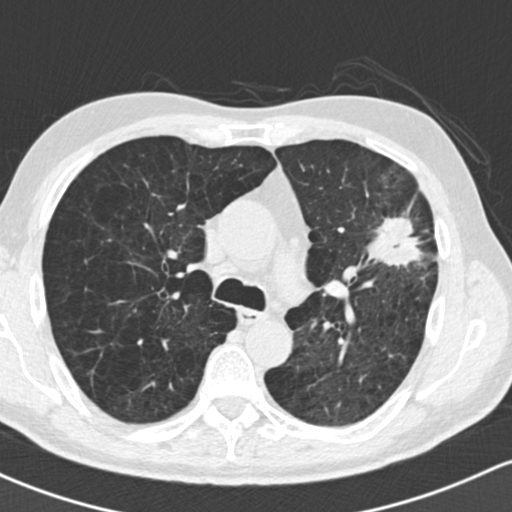
Chest CT (low-dose screening protocol), one axial image. First (baseline) screen. Lung window (W 1500 / L -600 HU). 2 mm slice thickness. Standard (soft-tissue) reconstruction kernel (B30f). Slice 62 of 162 in the series. Male participant, aged 61 years at enrolment. Former smoker at enrolment.
Expert reader's lesion annotation, box from (x=356, y=186) to (x=454, y=294) px. Screening reader's record for this exam (one nodule recorded; not confirmed to be the boxed lesion): non-calcified nodule or mass ≥4 mm, left upper lobe, 35 × 35 mm, spiculated (stellate) margins, soft tissue attenuation. Lung cancer was diagnosed 19 days after this screen: adenocarcinoma, NOS, left upper lobe, well differentiated (G1), stage IIIA (AJCC 6th edition), 45 mm at pathology.